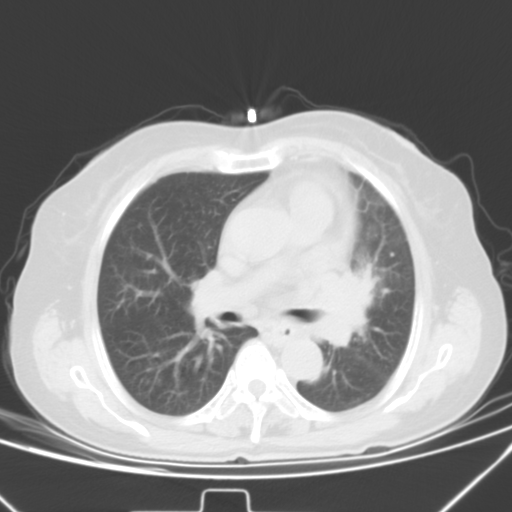
Chest CT, one axial slice. Slice 25 of 42 in the series (ordered by position). Lung window (W 1500 / L -600 HU). 5 mm slice thickness. 512 × 512 image matrix, field of view 331 × 331 mm. Patient: female, 59 years. Case-level facts recorded for this patient, not image findings: clinical TNM (as recorded): T3 N1 M0; histopathological grade: G3.
Structures marked on this image (rectangle marked by the reading radiologist):
- lung tumour (recorded histology: small cell carcinoma): bounding box [x1, y1, x2, y2] px = [308, 266, 377, 356]